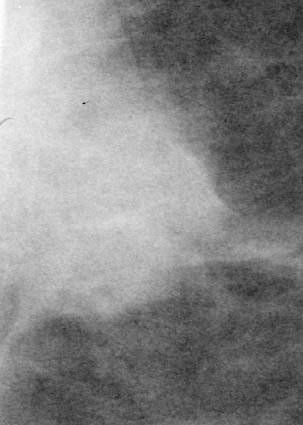
Crop from a digitized film mammogram around one marked abnormality; left breast; CC view; BI-RADS breast density category 3 (scale 1–4).
Marked abnormality: mass, shape irregular, margins spiculated; BI-RADS assessment category 4; pathology result (as recorded, not read from the image): malignant.